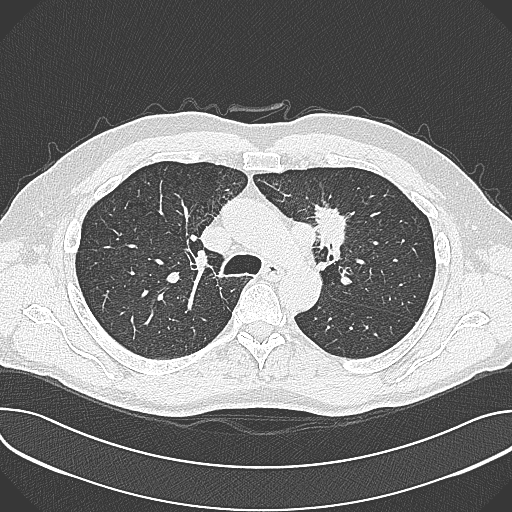
Chest CT (low-dose screening protocol), one axial image; first (baseline) screen; lung window (W 1500 / L -600 HU); 1 mm slice thickness; slice 104 of 361 in the series; 512 × 512 image matrix, field of view 380 × 380 mm. Male, age 59 years at enrolment. Current smoker at enrolment.
Expert reader's lesion annotation, box from (x=302, y=196) to (x=361, y=257) px. The screening reader recorded 2 non-calcified nodules or masses ≥4 mm on this exam; which of them this box marks is not recorded. Participant outcome: lung cancer diagnosed 21 days after this screen — non-small cell carcinoma, left upper lobe, poorly differentiated (G3), stage IIIA (AJCC 6th edition), 35 mm at pathology.